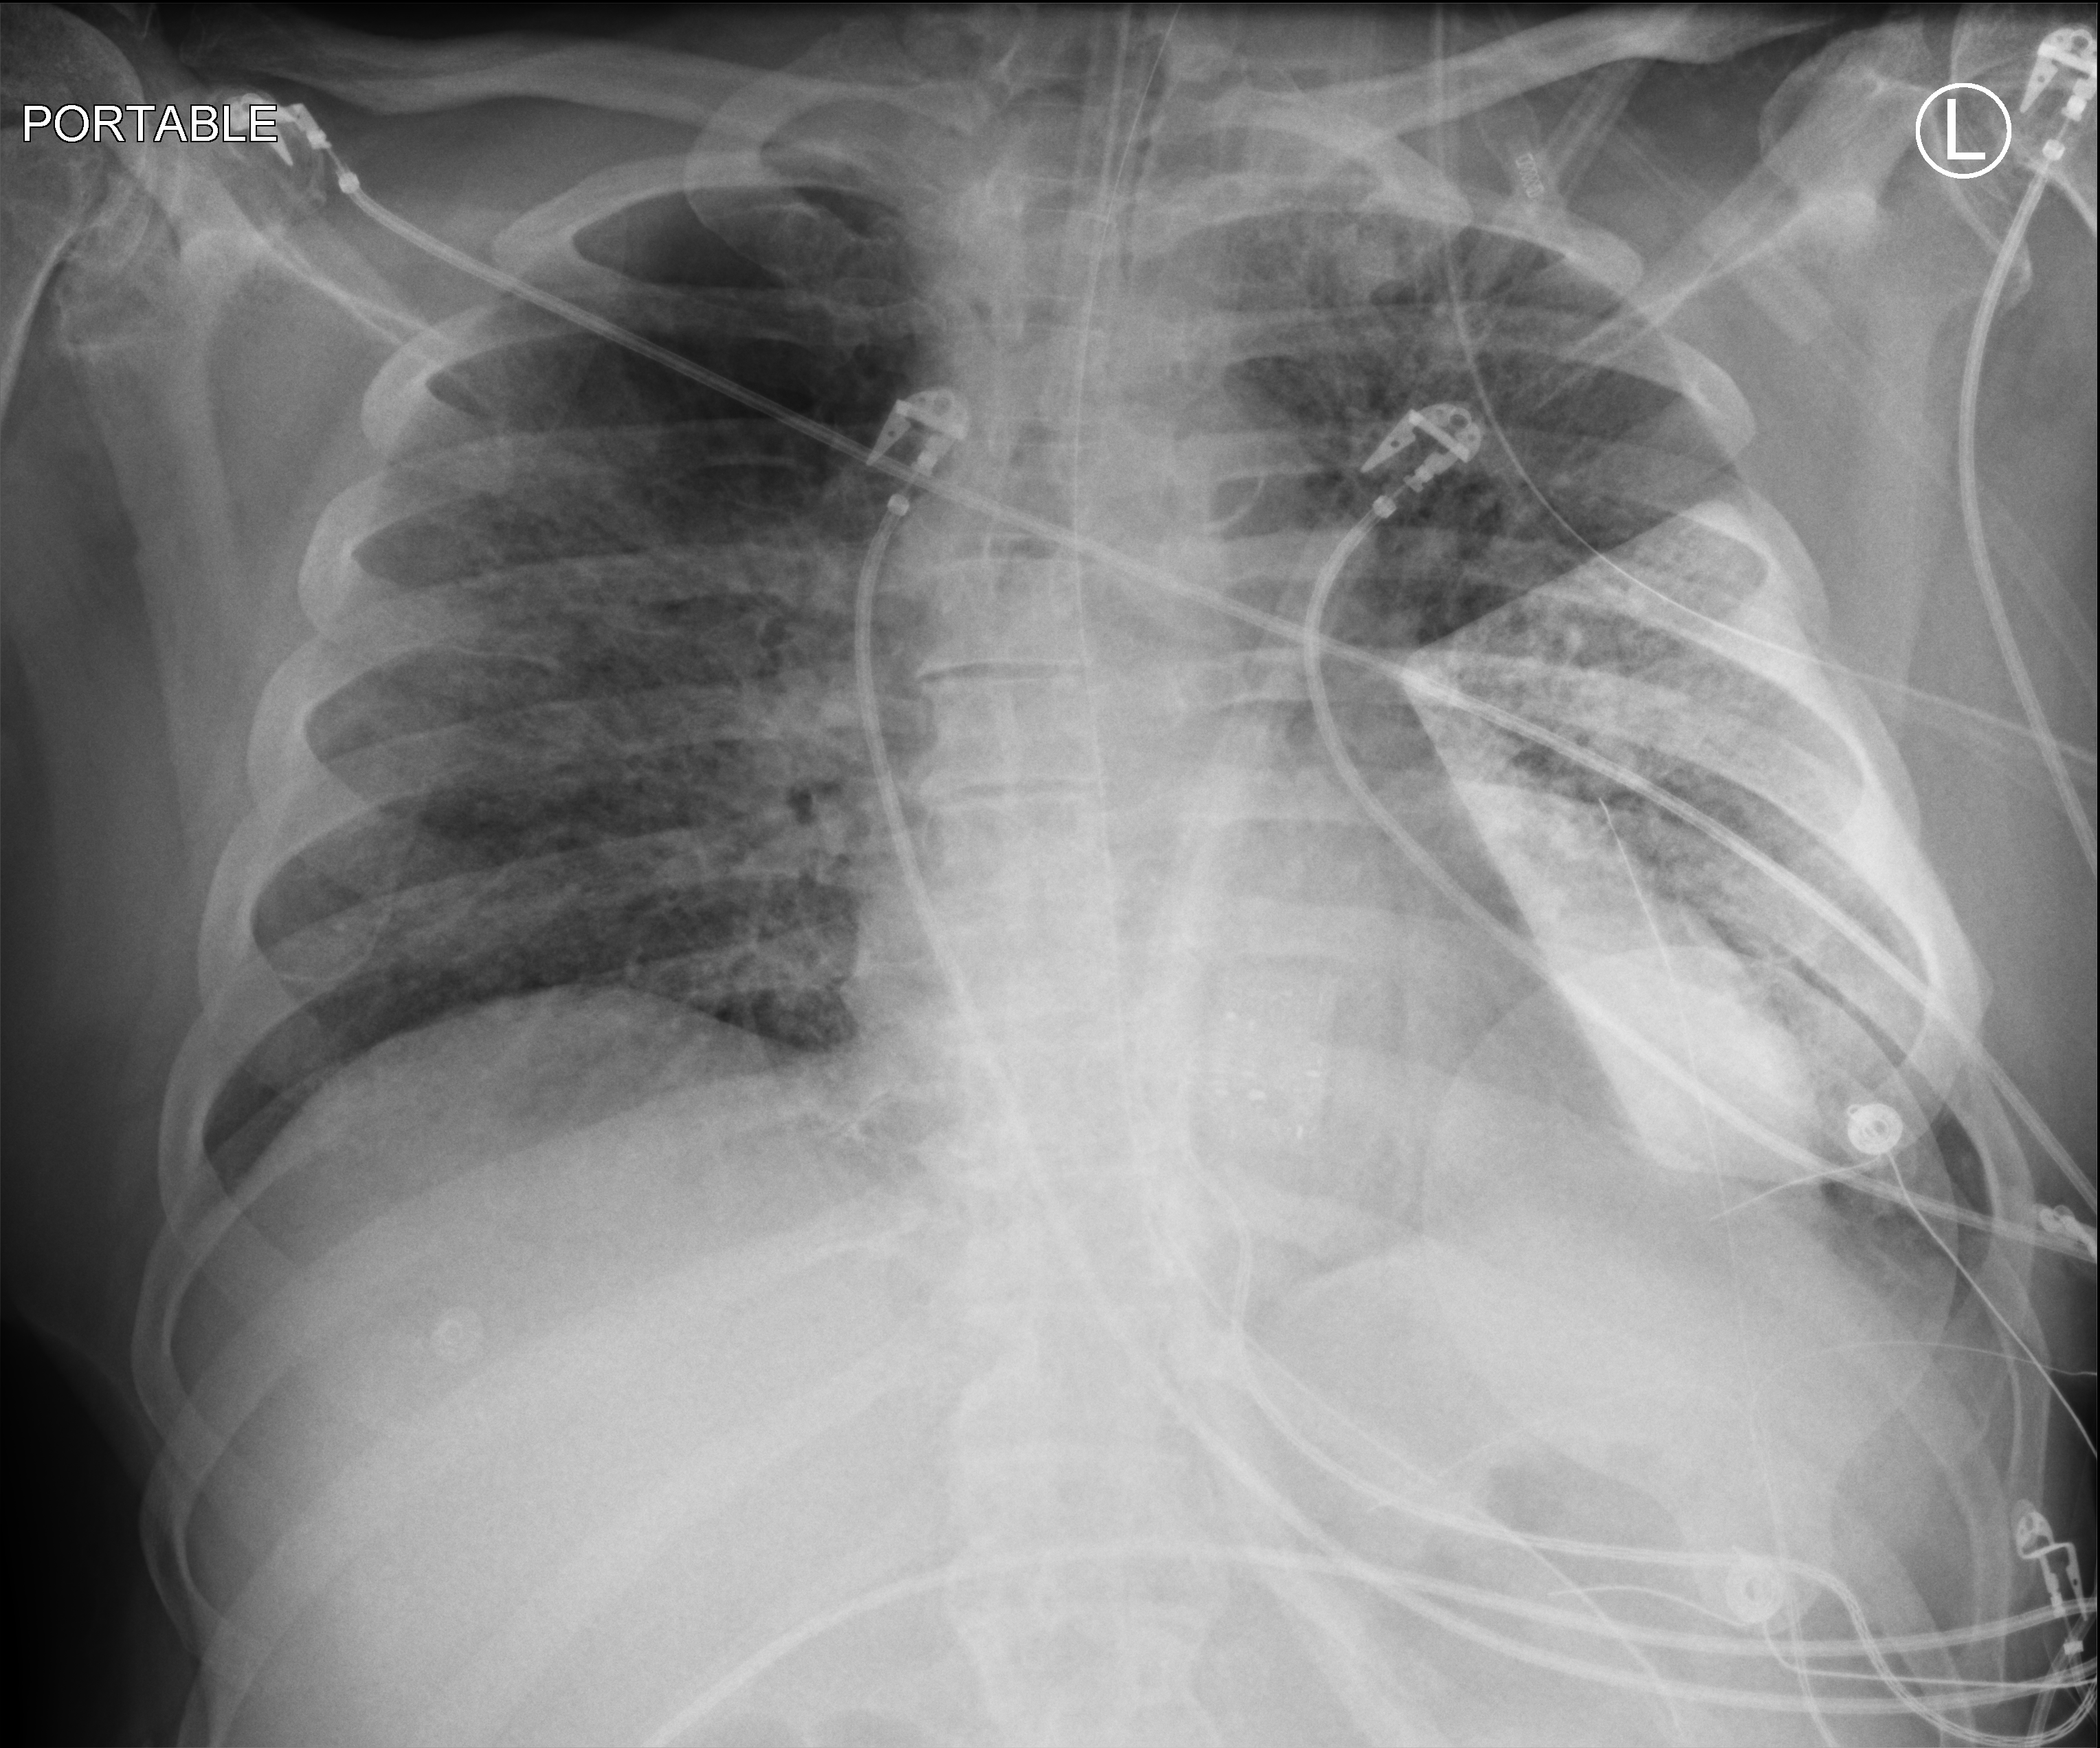
Portable chest radiograph, anteroposterior (AP) projection. Male patient hospitalised with COVID-19, age 60–74 years.
From the hospital-stay record, not from the radiograph (when in the stay this image was taken is not recorded): mechanically ventilated during this hospital stay: yes.